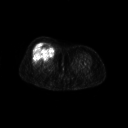
FDG PET of an extremity soft-tissue mass (from a PET/CT study), one axial slice; slice 39 of 267 in the series (ordered by position); 3.27 mm slice thickness; 128 × 128 image matrix, field of view 700 × 700 mm. Patient: female, 56 years. Case-level facts recorded for this patient, not image findings: histological type: malignant solitary fibrous tumor; grade: intermediate; site of the primary tumour: right thigh.
Outlined on this slice (expert contour drawn on MRI and transferred to this co-registered scan by the dataset authors):
- gross tumour volume including surrounding oedema: bounding box <32,42,56,60> (left, top, right, bottom; pixels)
- gross tumour volume (mass): <33,42,55,59>